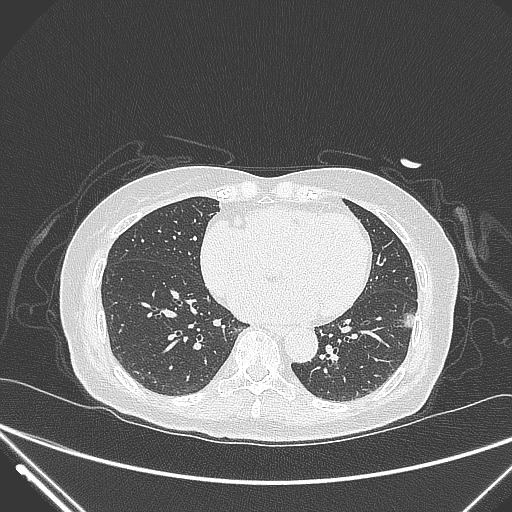
Chest CT, one axial slice; position 117 of 310 along the scan axis; lung window (W 1500 / L -600 HU); 512 × 512 image matrix, field of view 377 × 377 mm. Female patient, age 82 years. From the clinical record (not read from this slice): clinical TNM (as recorded): T1c N0 M0.
Outlined on this slice (bounding box drawn by a radiologist):
- lung tumour (recorded histology: adenocarcinoma): box from (x=398, y=303) to (x=420, y=331) px